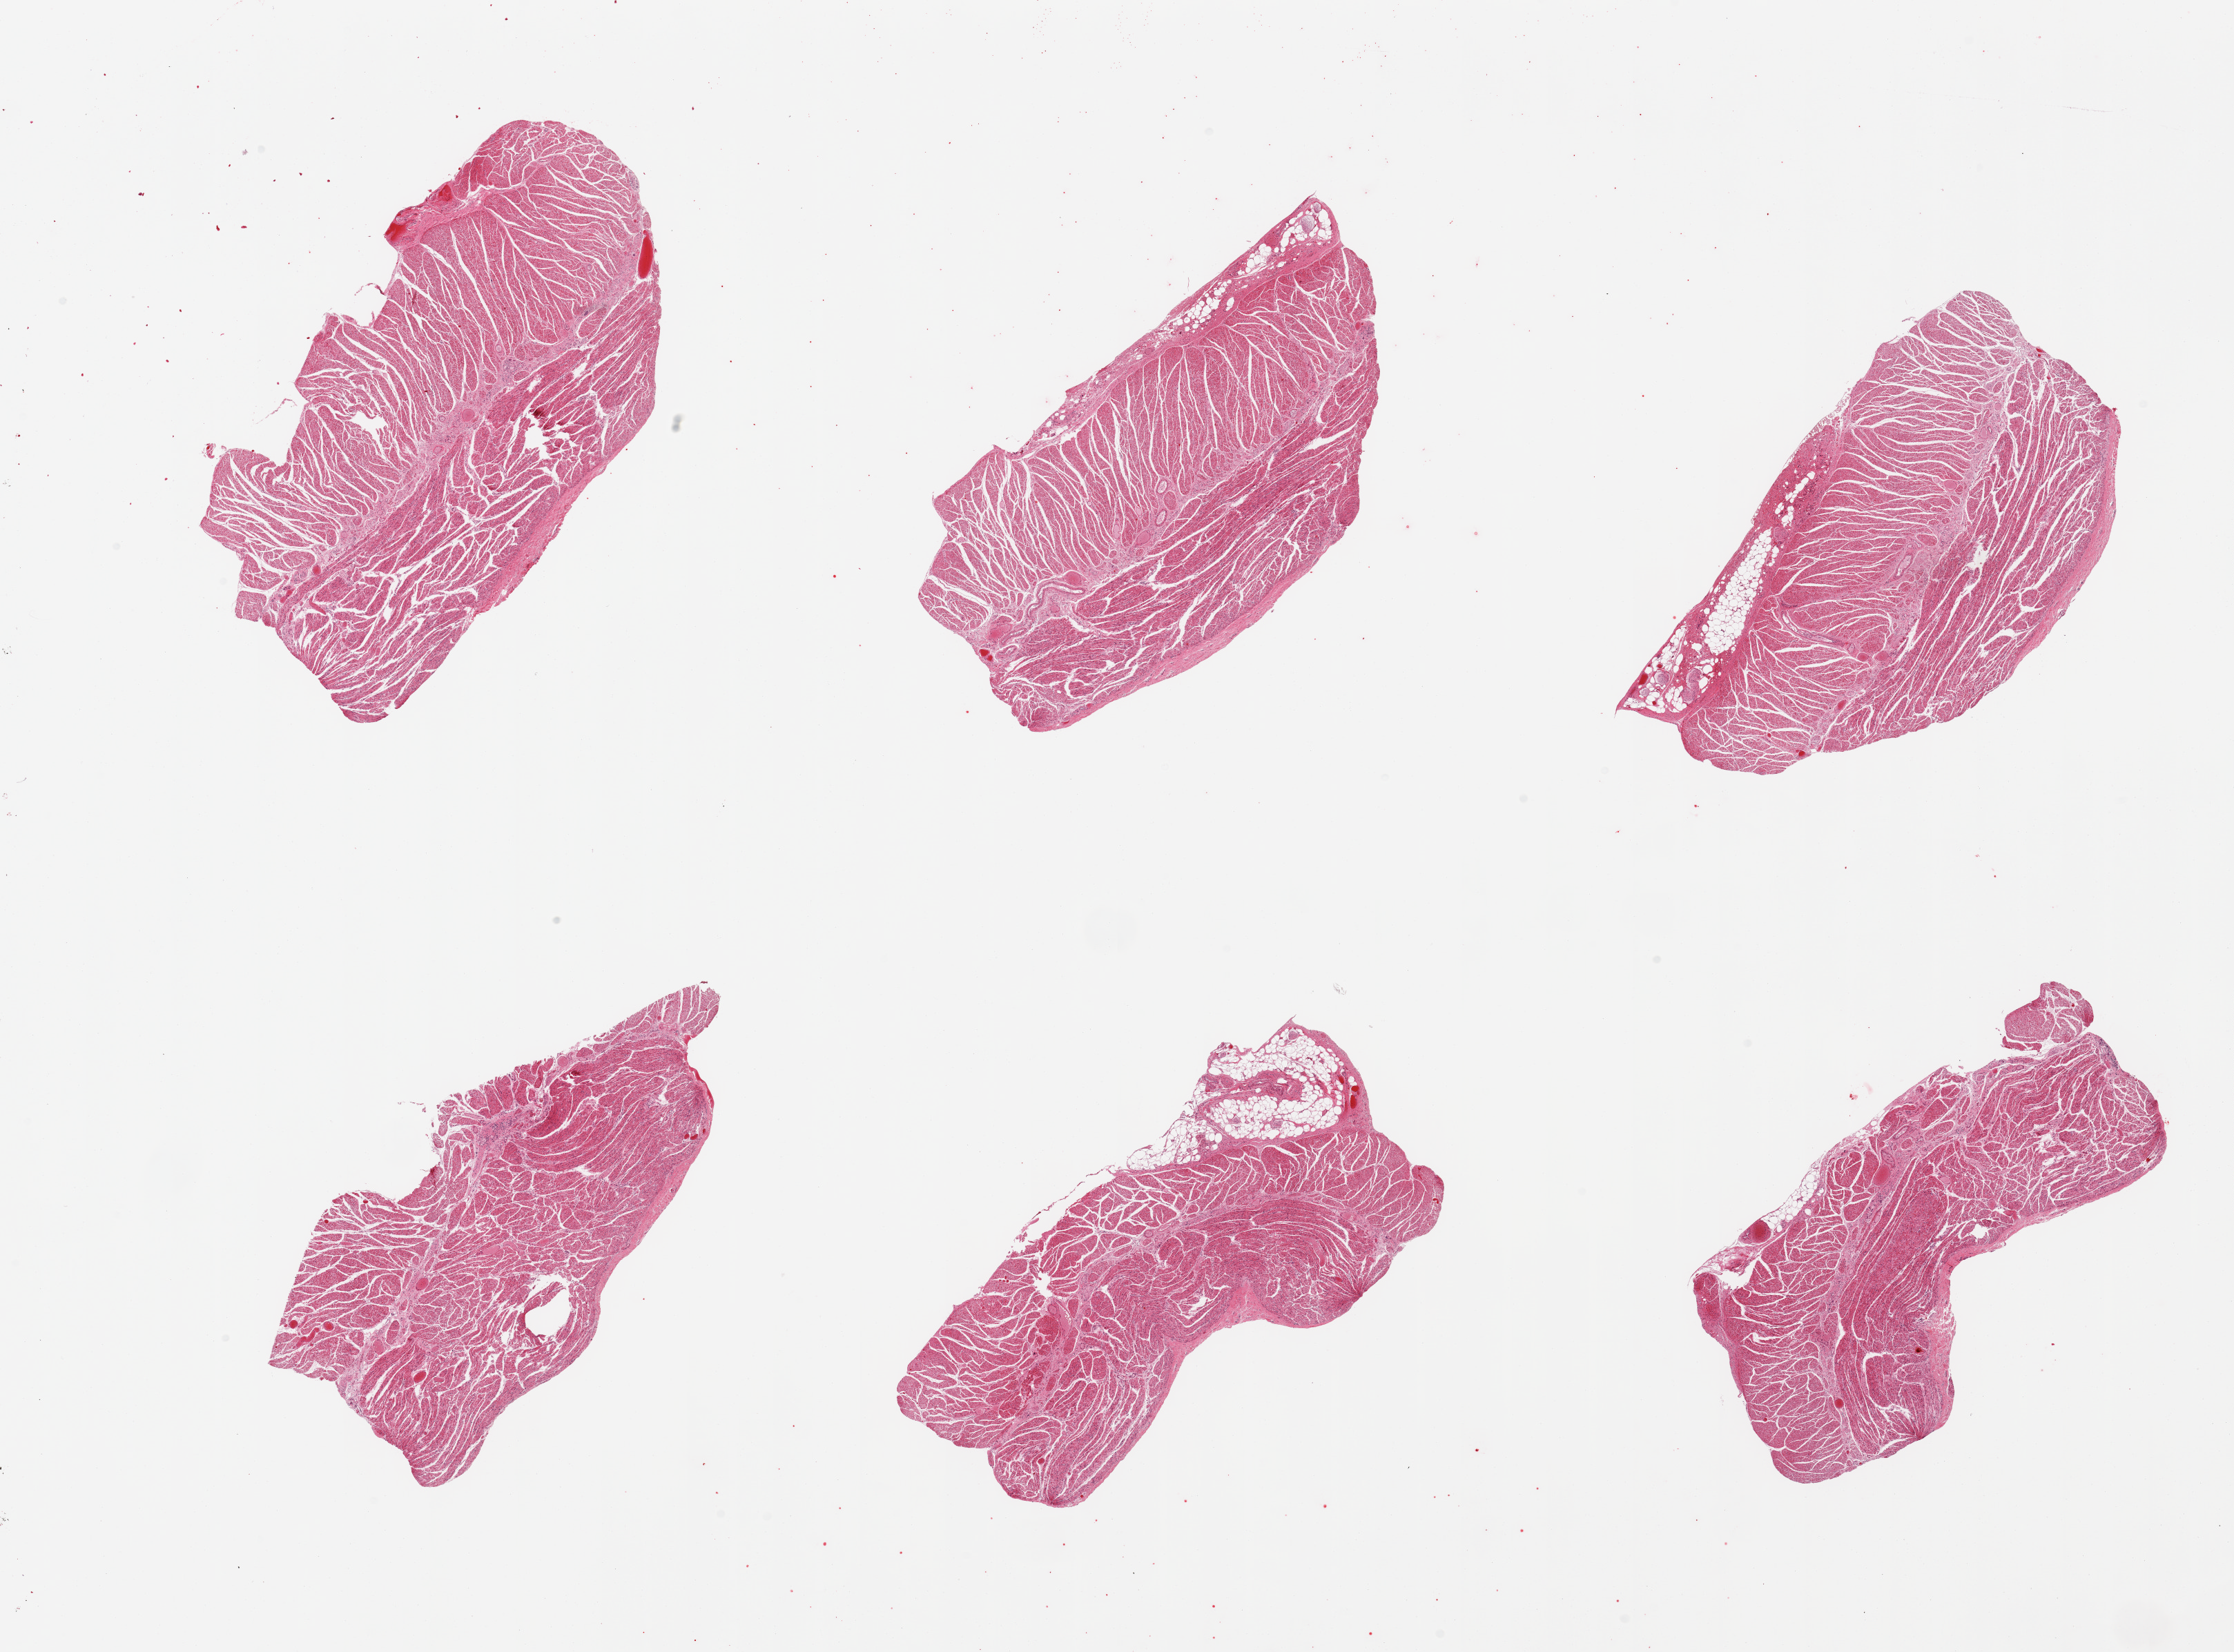
Hematoxylin and eosin (H&E) whole-slide image, brightfield, low-resolution overview of the scanned area, about 25.6 x 18.9 mm (from a 20x scan). PAXgene-fixed paraffin-embedded (PFPE) section. Sampled site (target tissue): gastroesophageal junction. Tissue donor sample. Donor: female.
Review note (as recorded): 6 pieces; target muscularis present, small amounts of fat/nerve attached to several pieces.